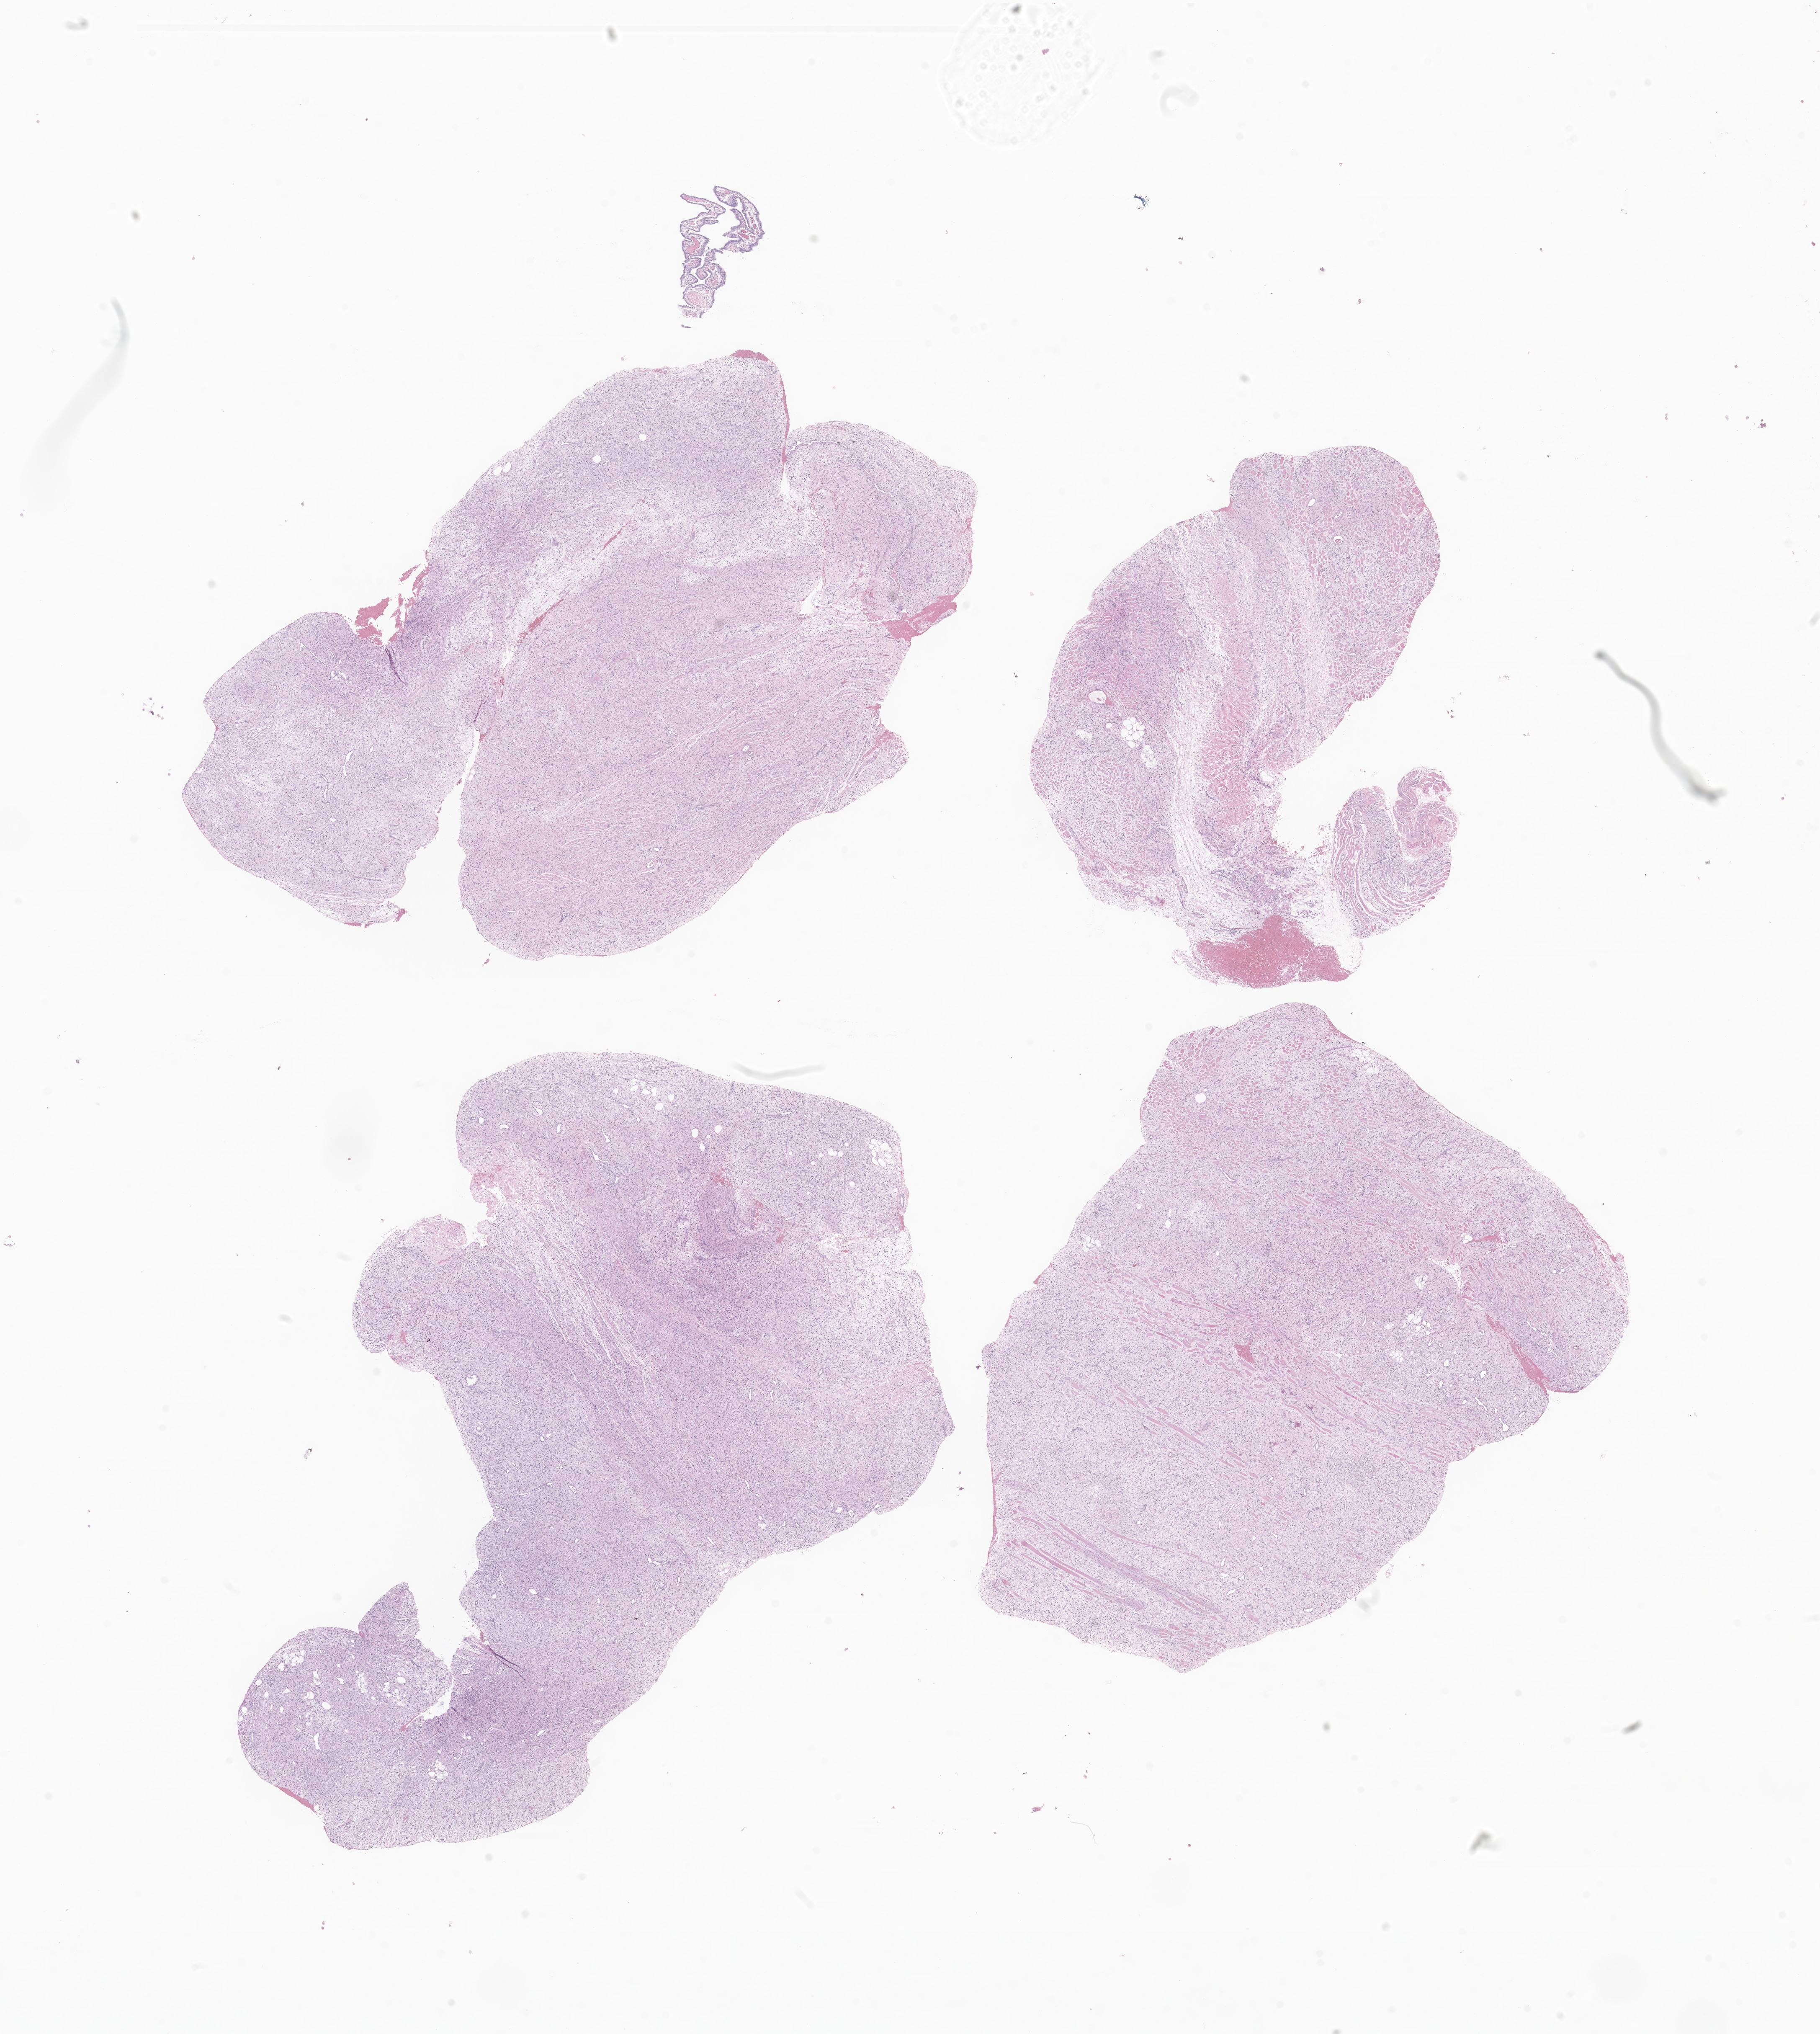
Digitized hematoxylin and eosin (H&E)-stained section of tumor tissue from the soft tissue of lower extremity, shown as a low-resolution overview of the whole scanned area (about 18.3 x 20.5 mm); formalin-fixed paraffin-embedded section. Patient male; age 99 days.
Diagnosis (ICD-O-3 morphology term): Infantile fibrosarcoma.